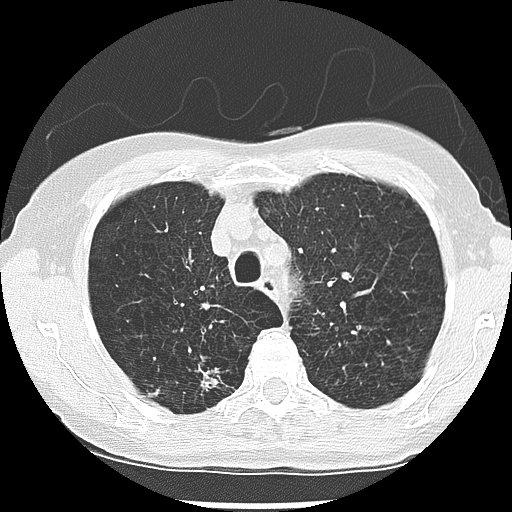
Low-dose screening chest CT, one axial slice; slice 211 of 265 in the series (ordered by position); reconstruction kernel LUNG; lung window (W 1500 / L -600 HU); 2.5 mm slice thickness; 512 × 512 image matrix.
Outlined on this slice (outlined manually by an expert reader):
- lesion 1 (nodule, upper lobe of right lung): bounding box [x1, y1, x2, y2] px = [202, 370, 218, 390]